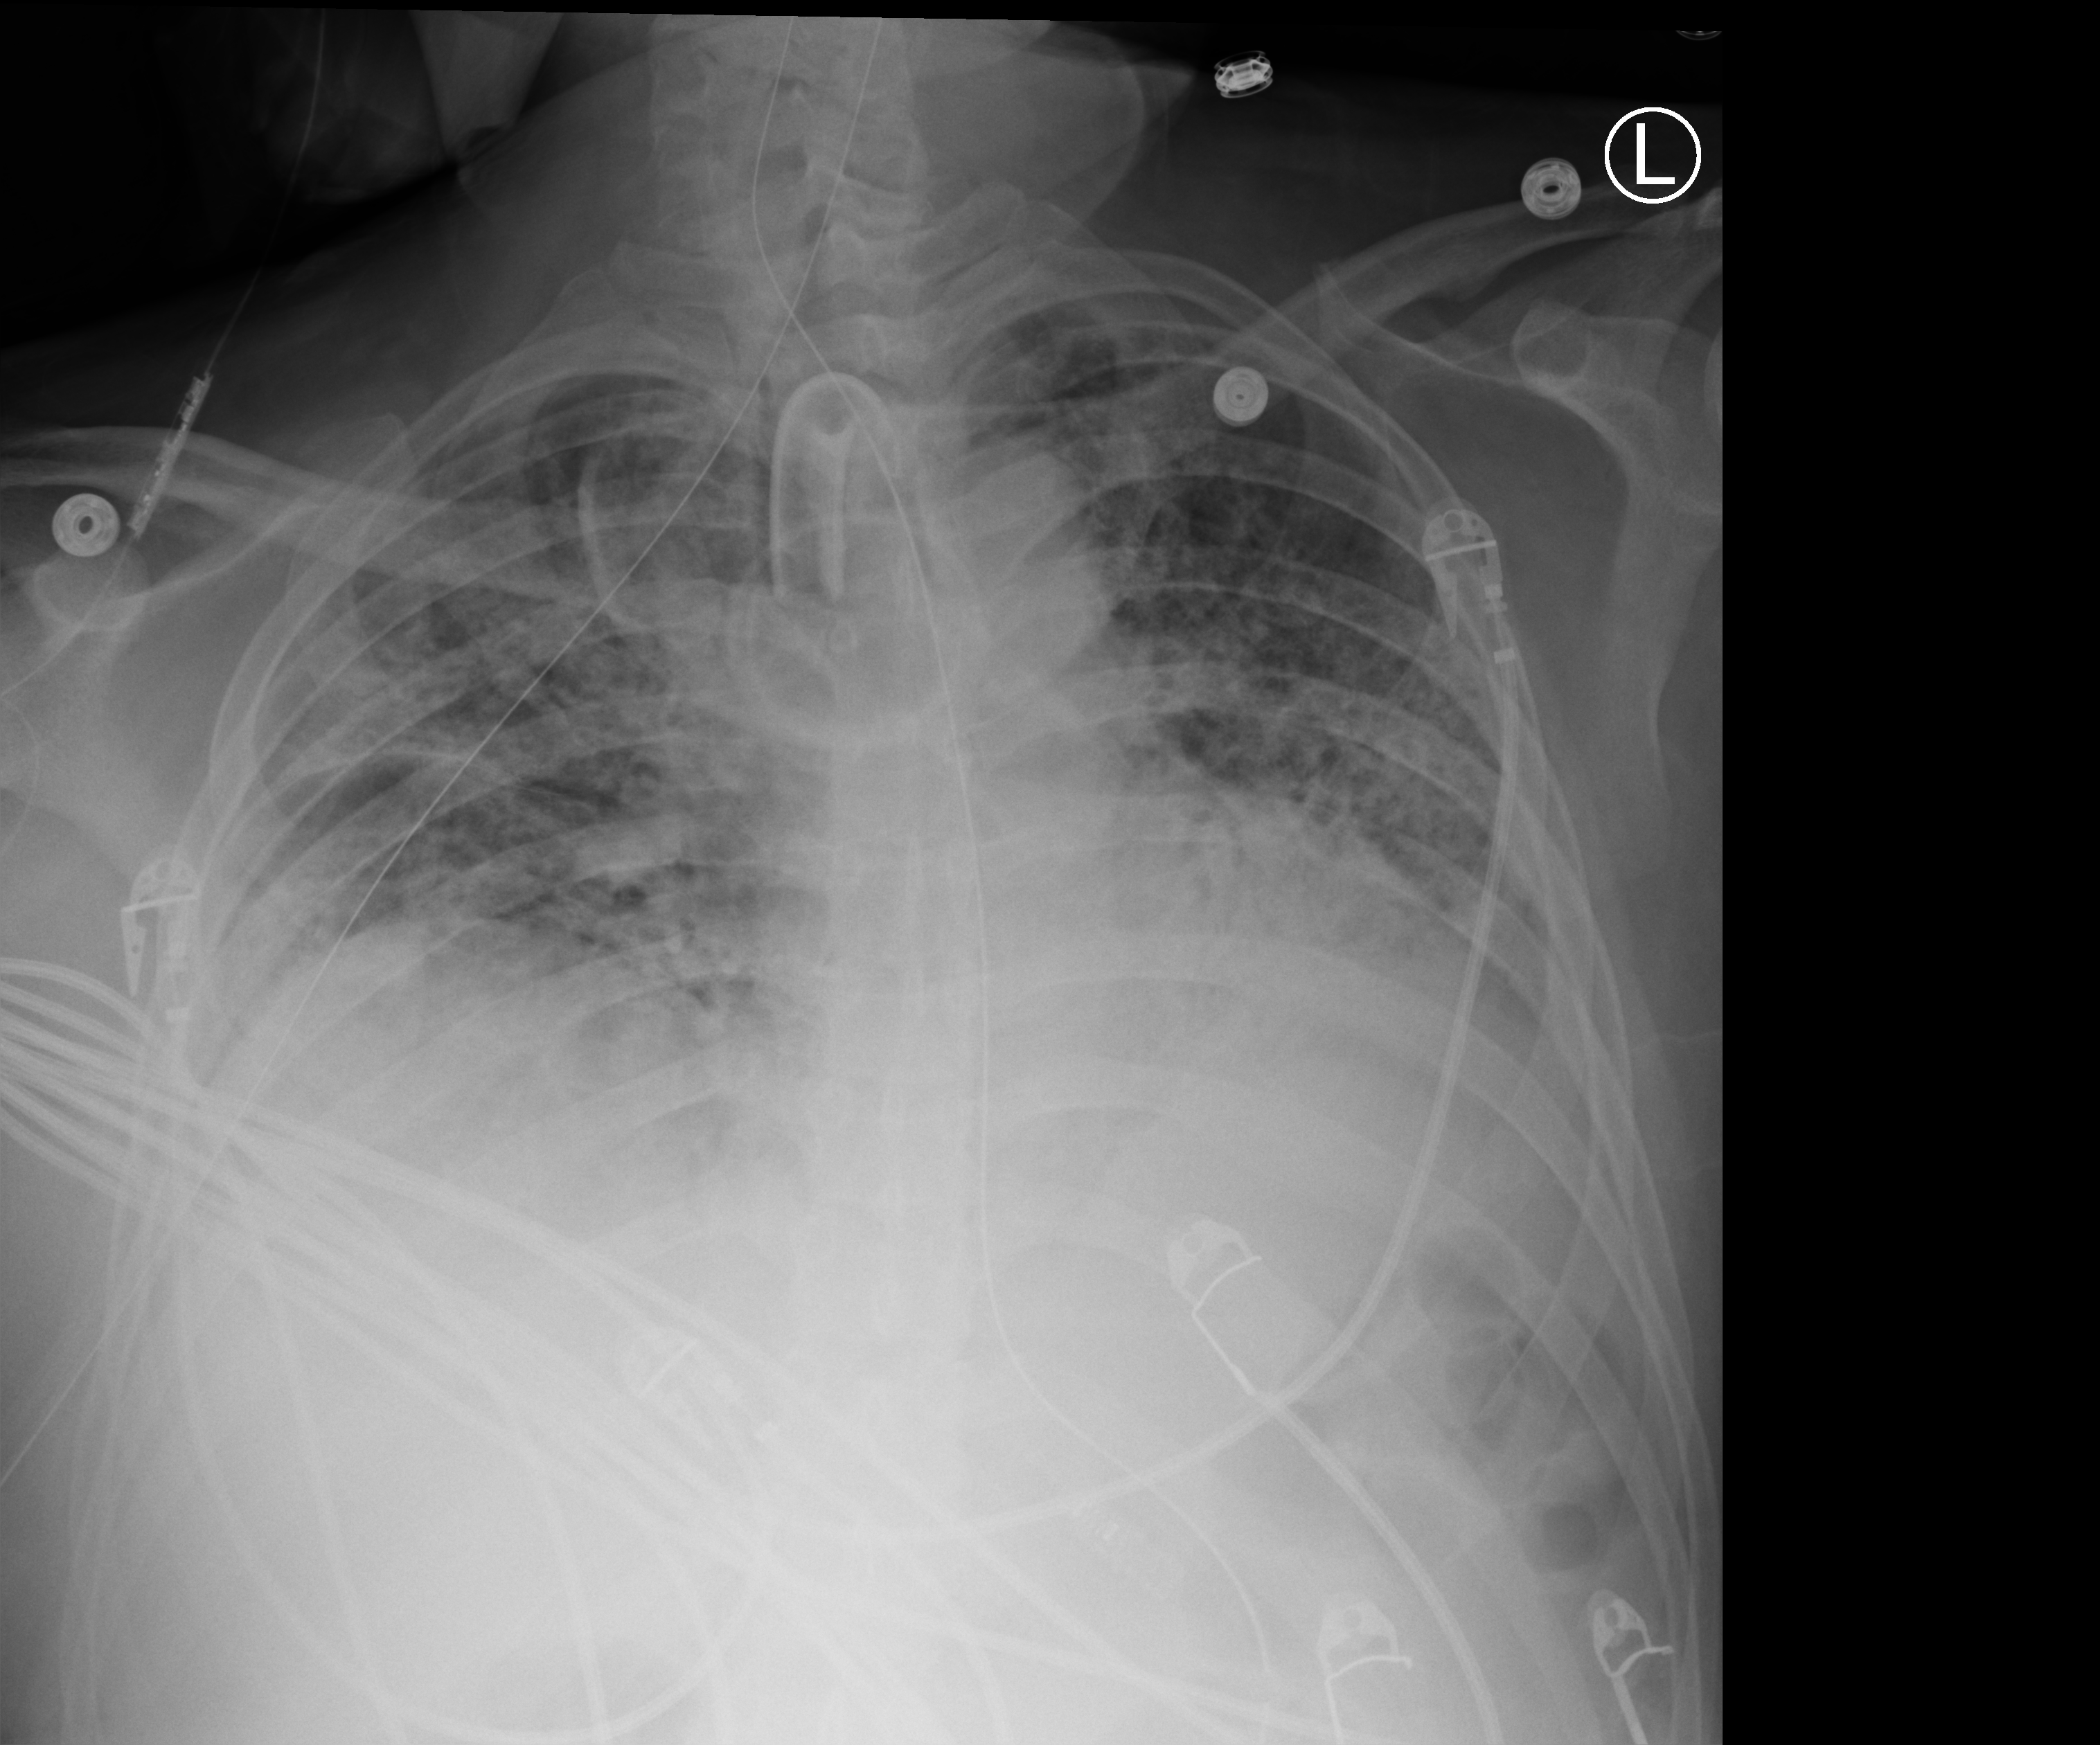
Portable chest radiograph, anteroposterior (AP) projection. Male patient hospitalised with COVID-19, age 18–59 years.
From the hospital-stay record, not from the radiograph (when in the stay this image was taken is not recorded): diabetes (admission record): no; mechanically ventilated during this hospital stay: yes.